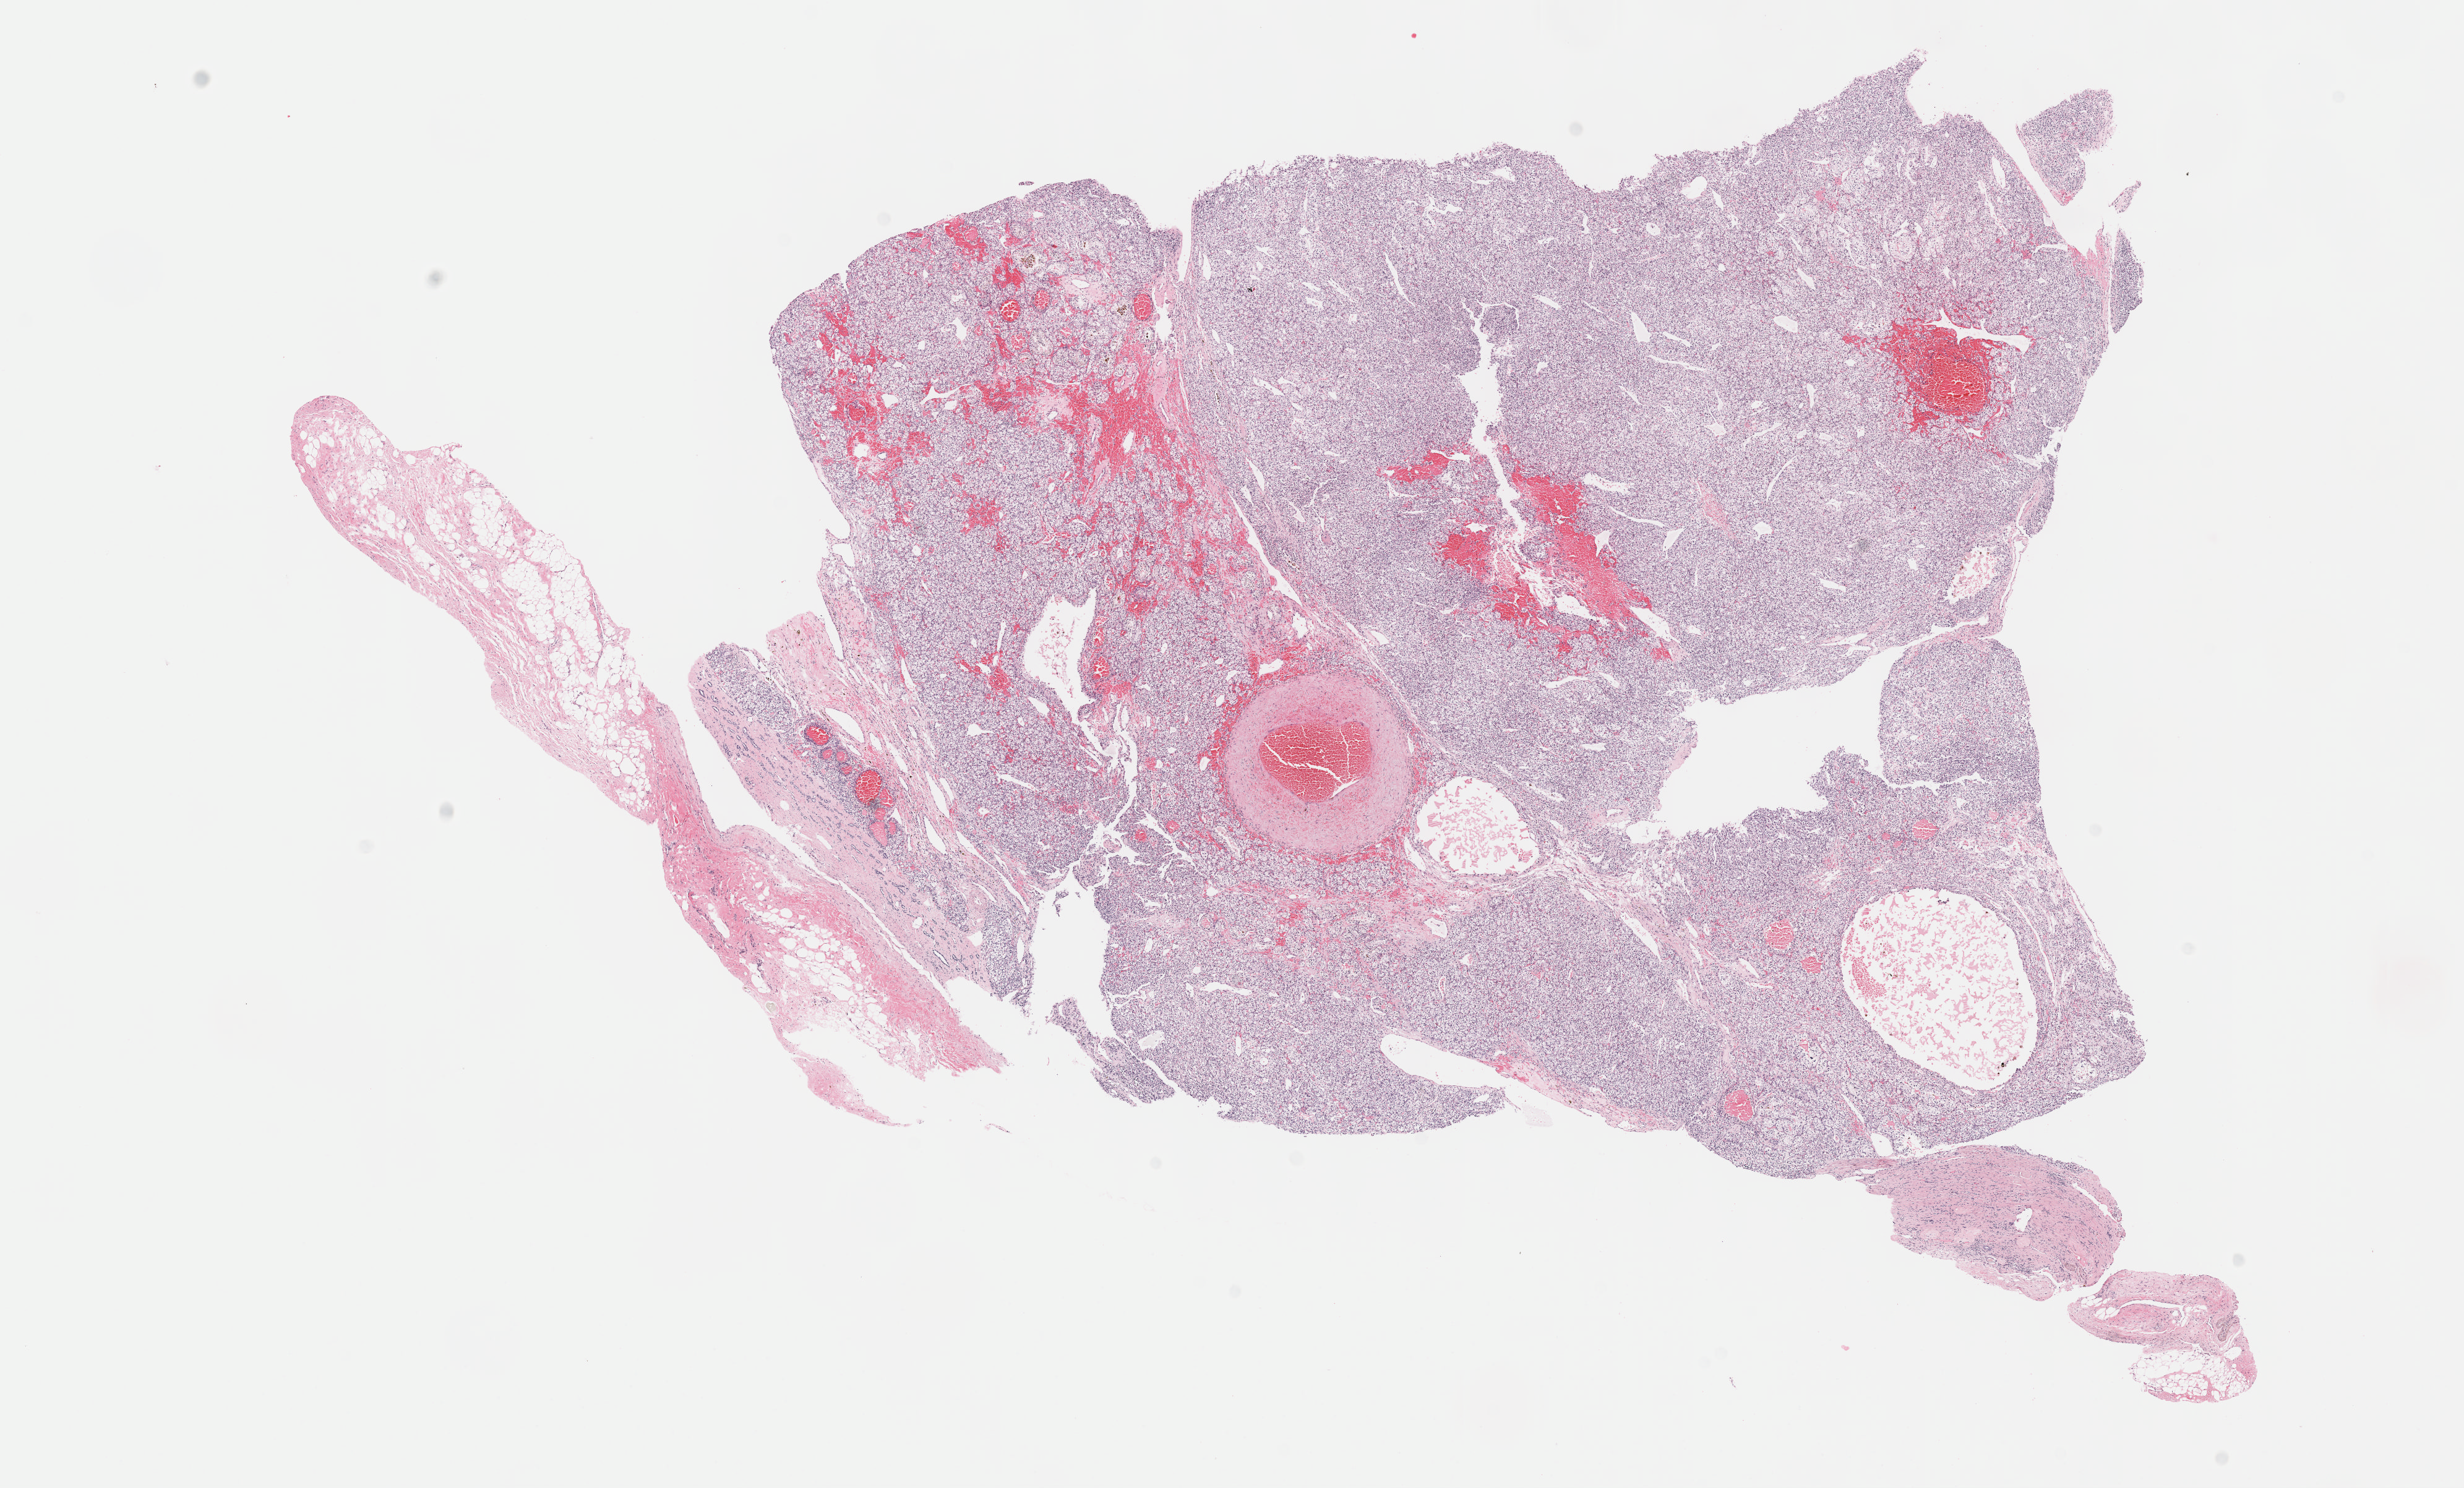
Digitized H&E-stained tissue section (whole slide), whole scanned area (about 16.1 x 9.7 mm, acquisition: 40x scan) shown as a low-resolution overview, formalin-fixed paraffin-embedded (FFPE) diagnostic section, kidney, primary tumour sample. Patient: male, age at initial diagnosis 72 years. Histologic grade: G2 (moderately differentiated).
TNM: T1a NX M0. Pathologic diagnosis: Clear cell adenocarcinoma, NOS. Laterality: left. AJCC pathologic stage: I.